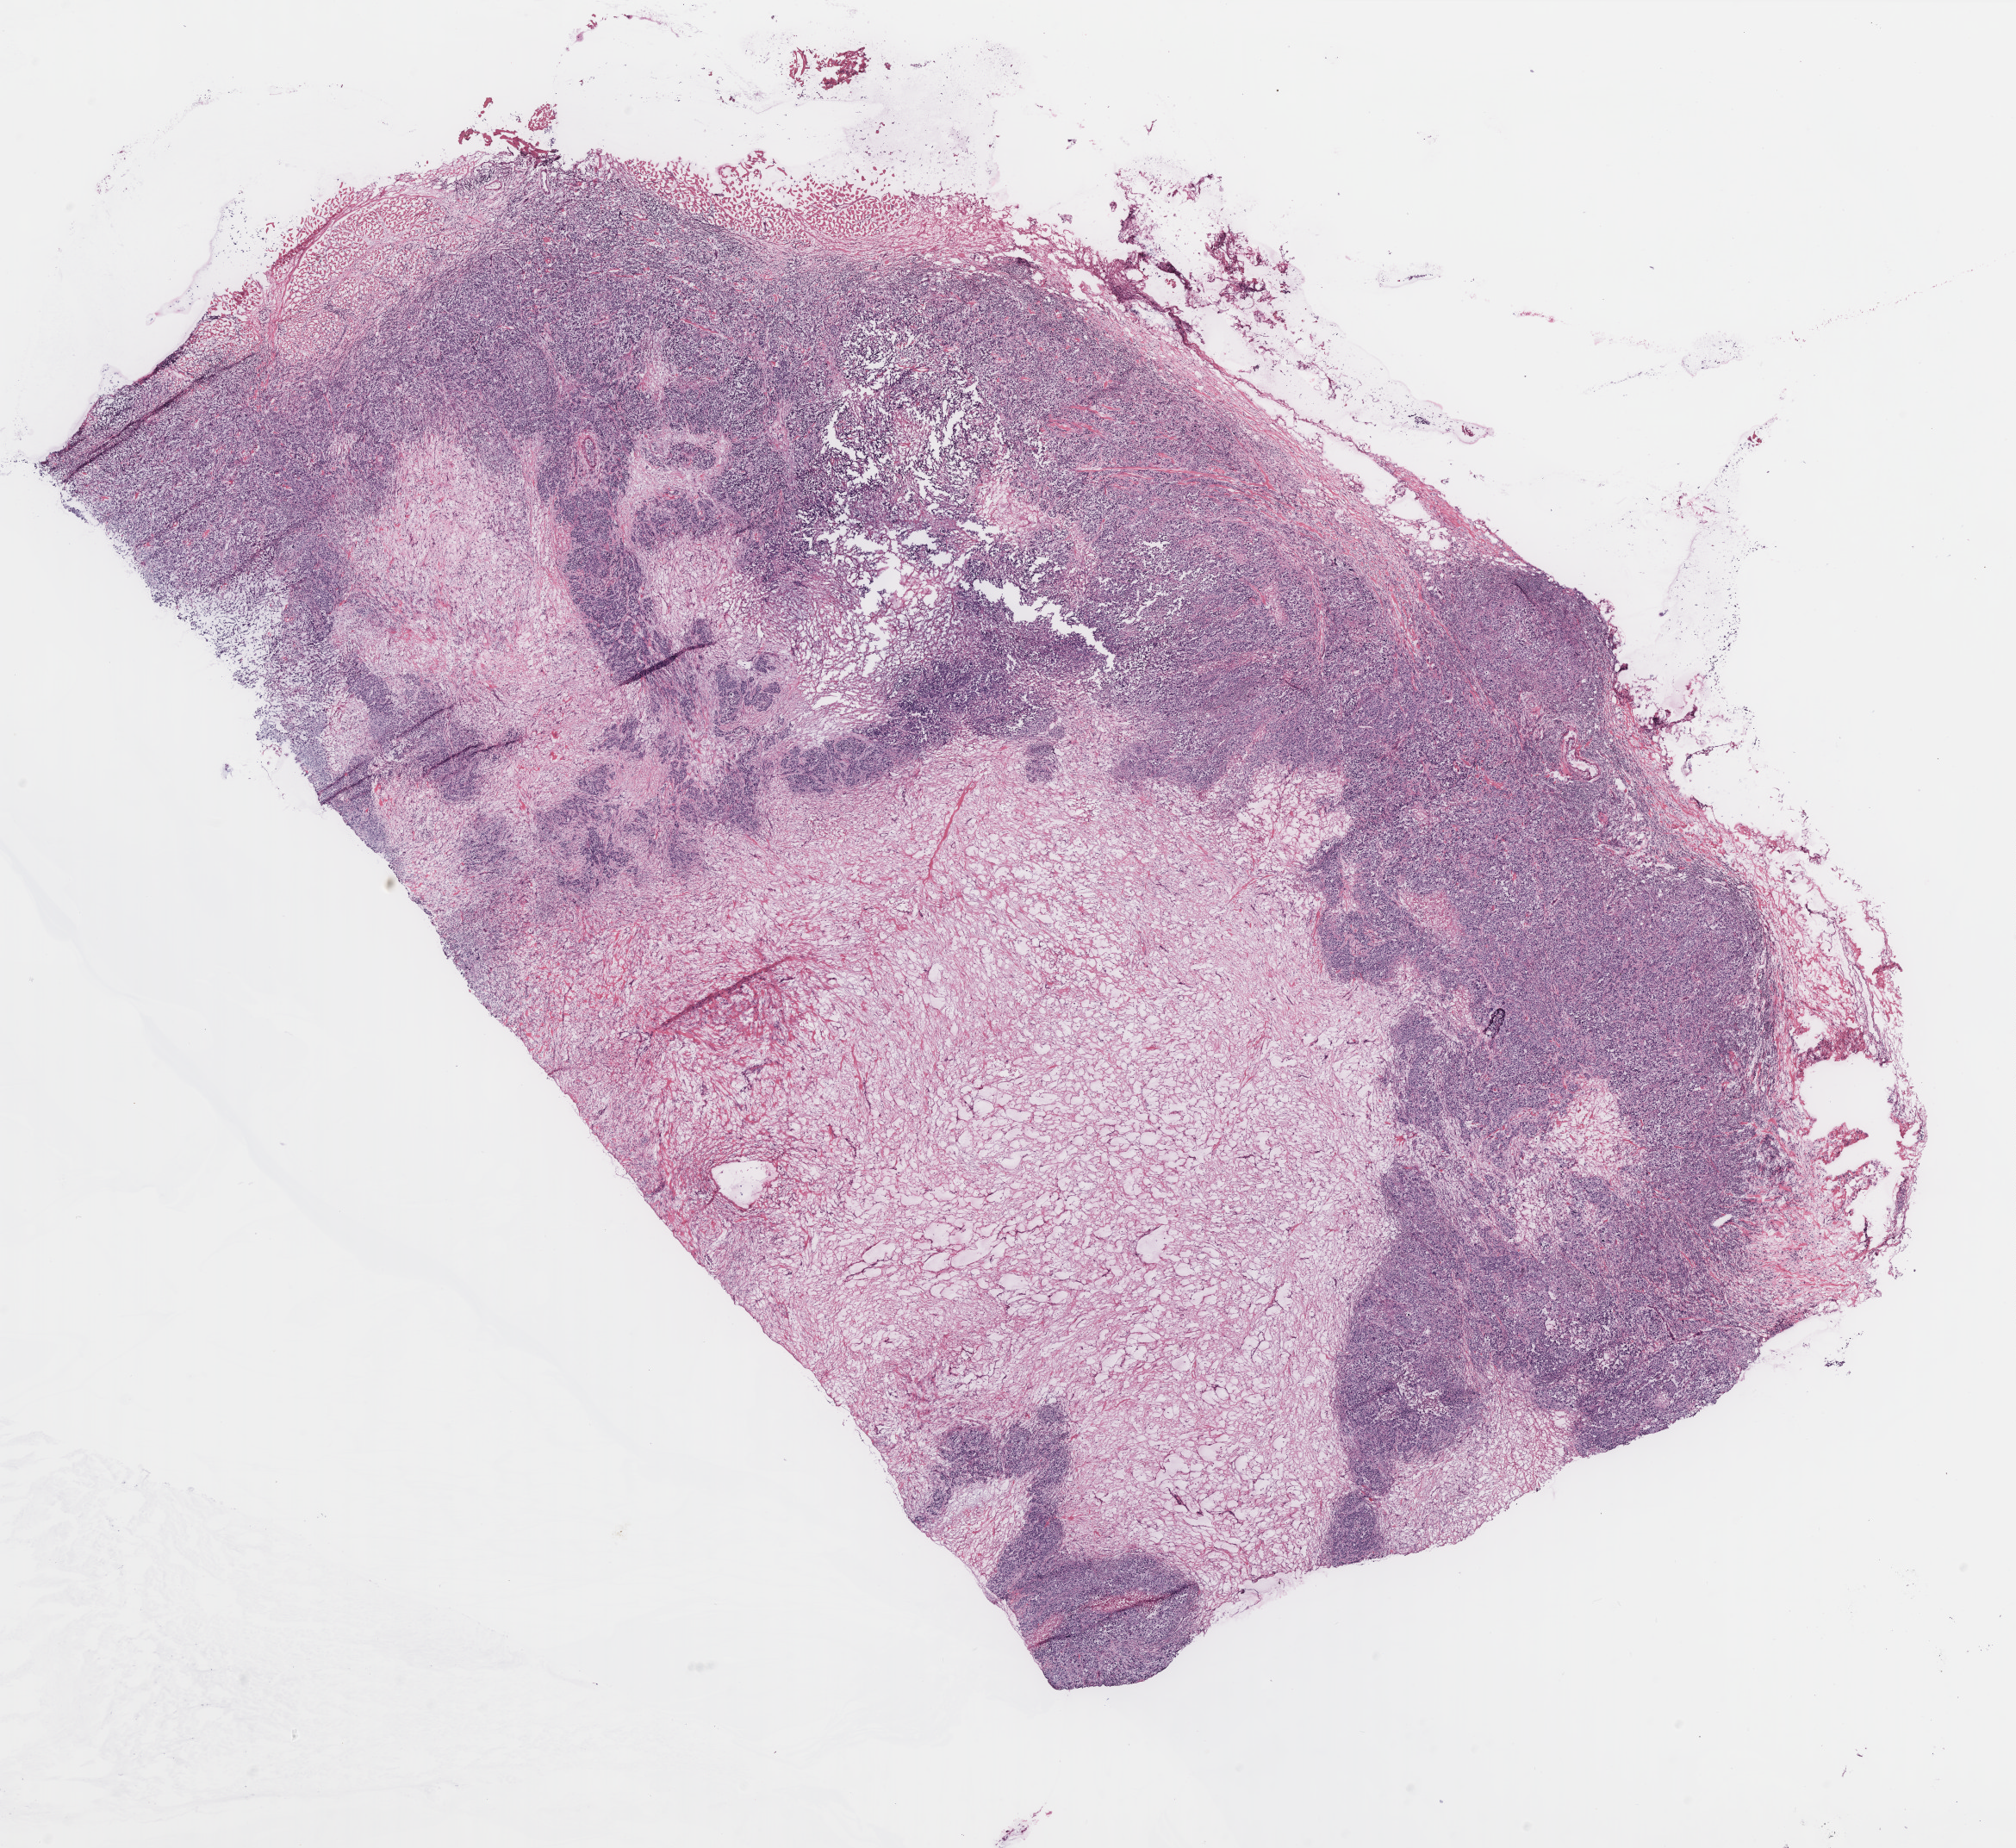
Whole-slide histology image, H&E — shown as a low-resolution overview of the whole scanned area (about 18.7 x 17.2 mm, slide scanned at 40x); breast, tissue type not recorded. Patient: female, age 68 years.
• patient diagnosis: Infiltrating duct carcinoma, NOS